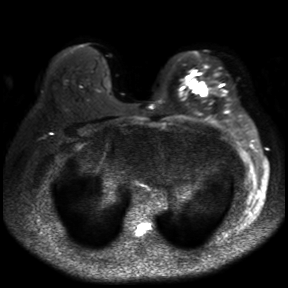
Breast MRI, one axial slice; position 20 of 30 along the scan axis; diffusion-weighted series; image 2 of 4 stored at this slice position (different b-values; order by instance number); 3 T; 4 mm slice thickness; 288 × 288 image matrix, field of view 360 × 360 mm. Female patient.
Structures marked on this image (expert manual segmentation):
- tumour on diffusion-weighted imaging: bounding box (x1, y1, x2, y2) in pixels: (189, 79, 208, 96)